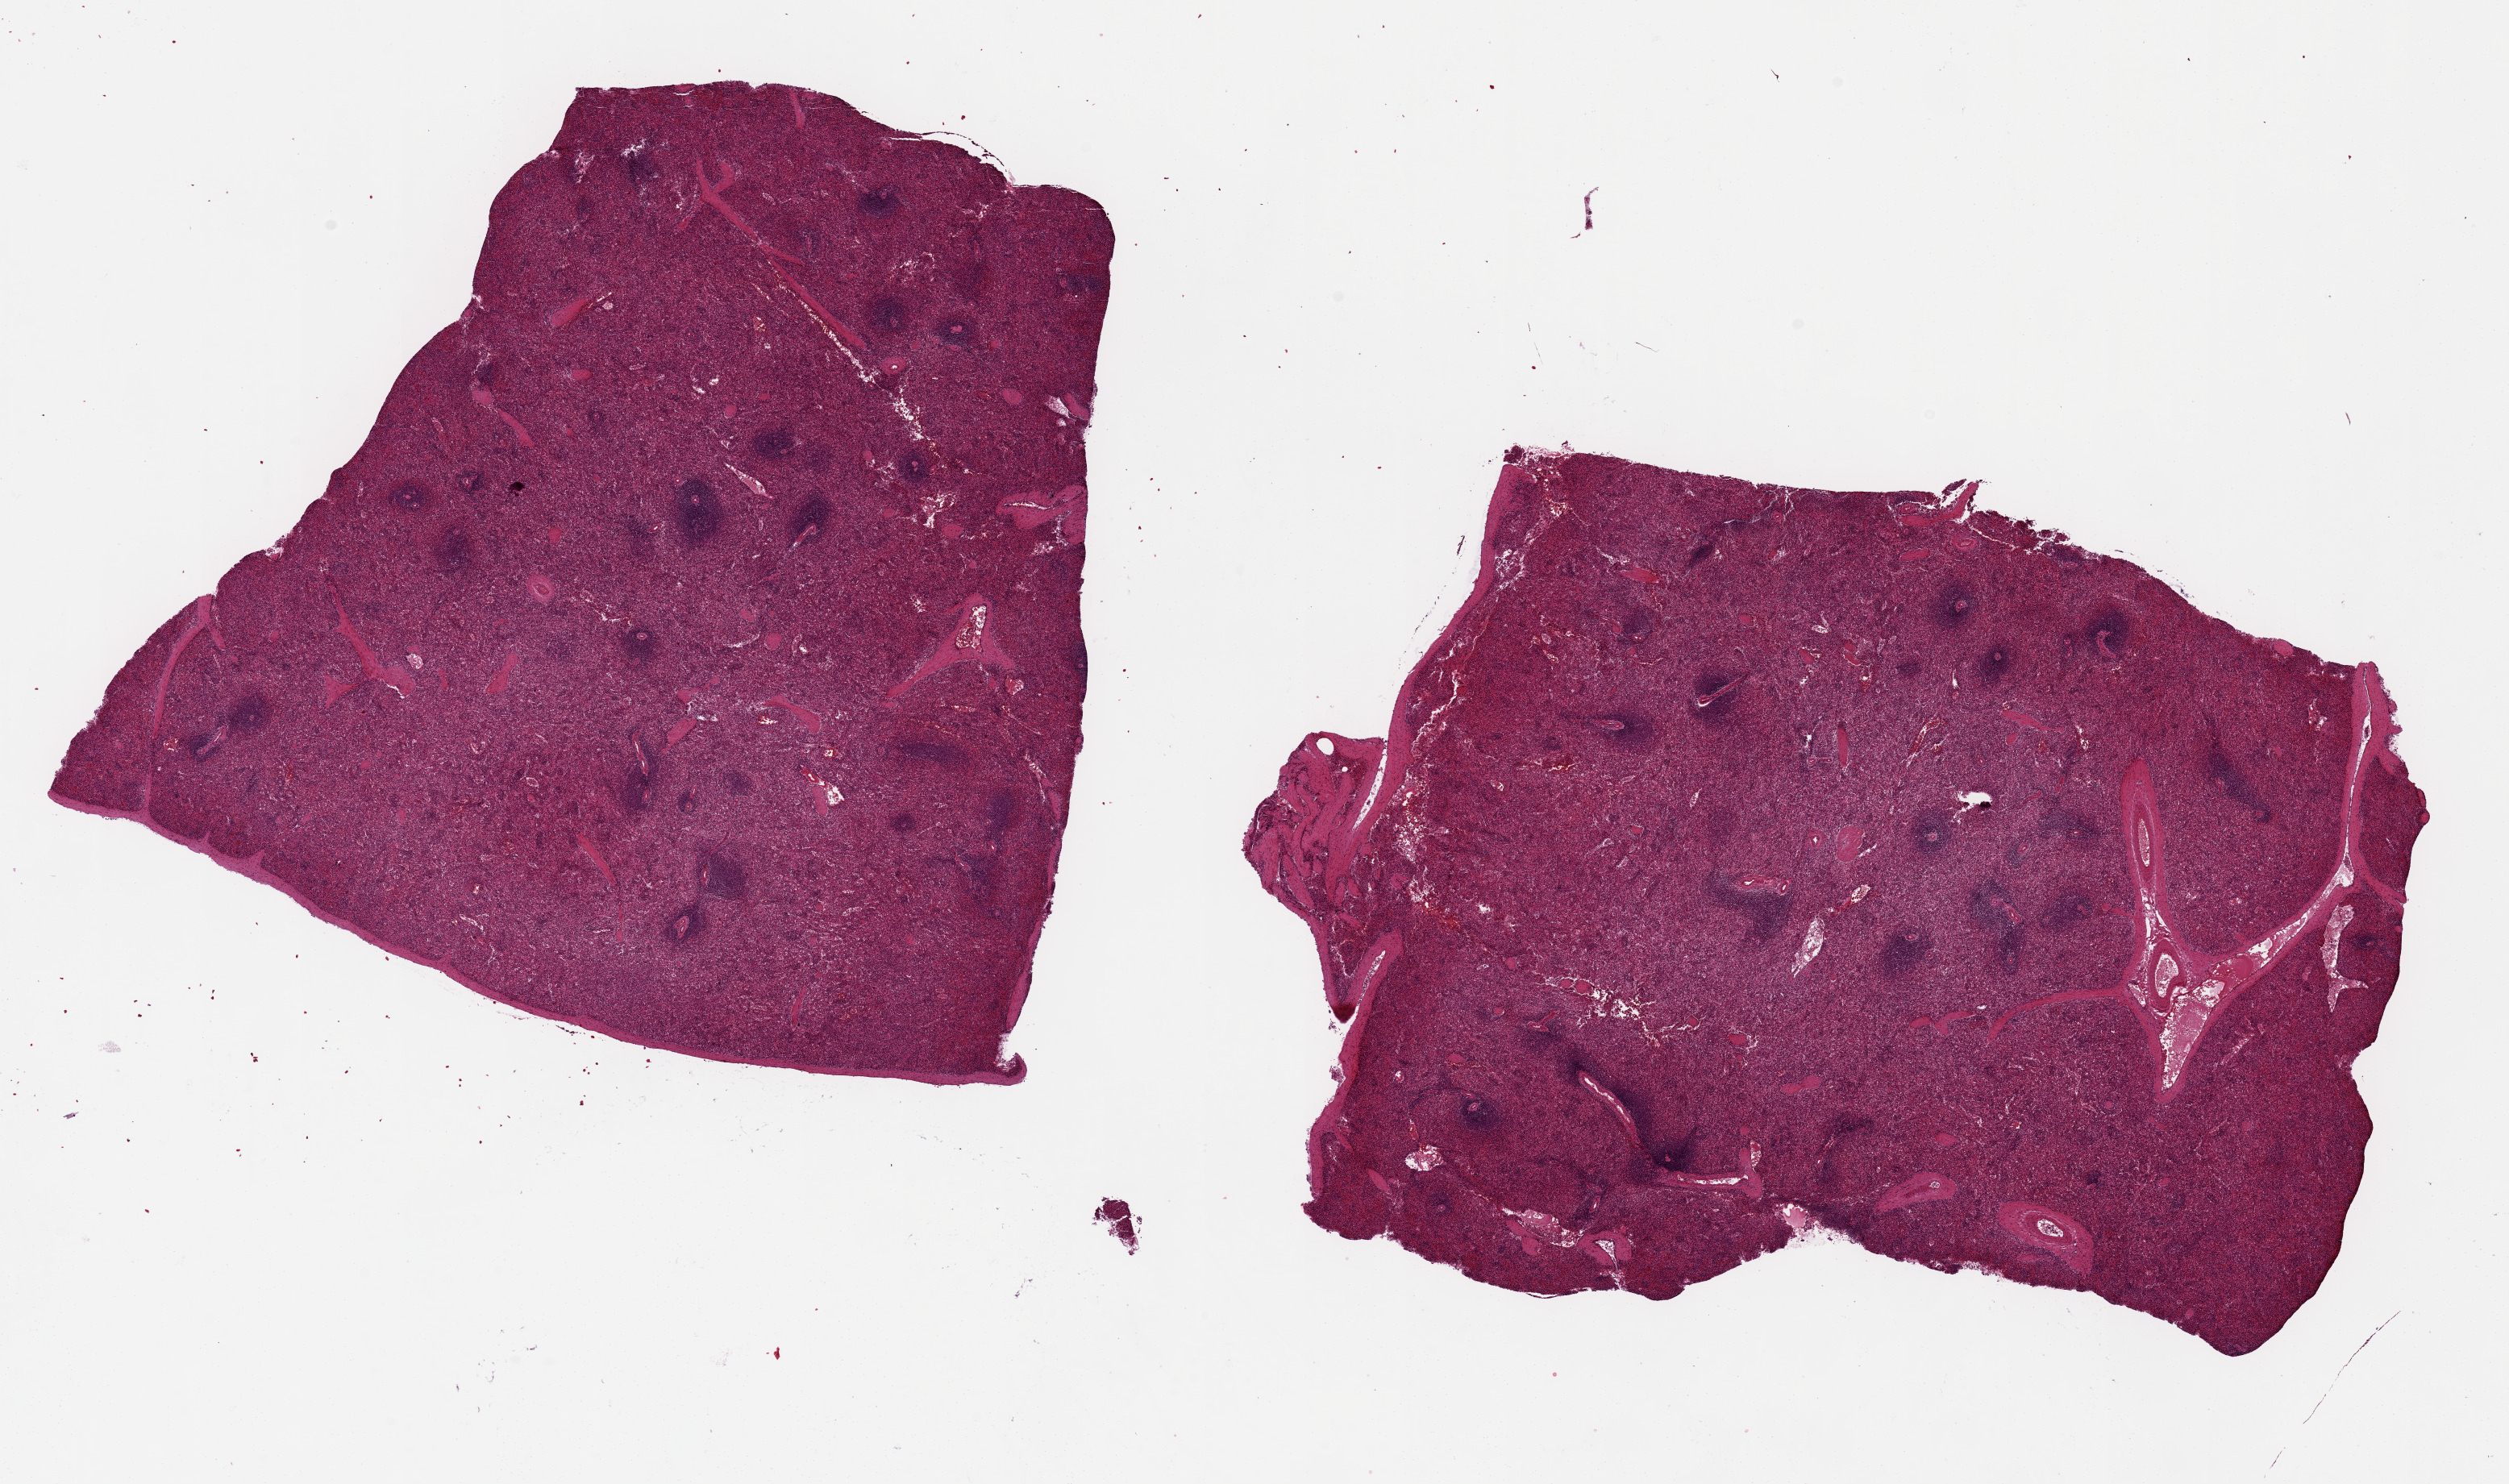
Digitized haematoxylin and eosin-stained section — shown as a low-resolution overview of the whole scanned area (about 24.6 x 14.6 mm, slide scanned at 20x), PAXgene-fixed, paraffin-embedded tissue, target tissue: spleen, donor tissue sample.
Pathologist's review note for this sample: 2 ~9x7.5mm aliquots.